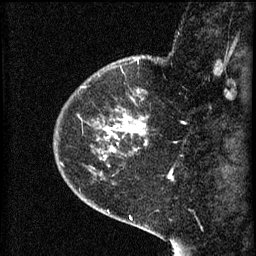
Breast MRI (dynamic contrast-enhanced), one sagittal slice. Slice 15 of 60 in the series (ordered by position). 3 images stored at this slice position (order not interpretable as contrast timing). 1.5 T. TE 4.2 ms, TR 8.2 ms. 256 × 256 image matrix. Female patient, age 44 years.
Annotated regions visible in this slice (semi-automatic segmentation, software-assisted and operator-edited):
- analysis volume of interest (the breast-tissue region the enhancement analysis was run in; not a lesion): box from (x=73, y=82) to (x=150, y=165) px
- tumour enhancement mask (voxels above the 70 % enhancement threshold inside the analysis volume of interest): (x=105, y=90)–(x=148, y=153)